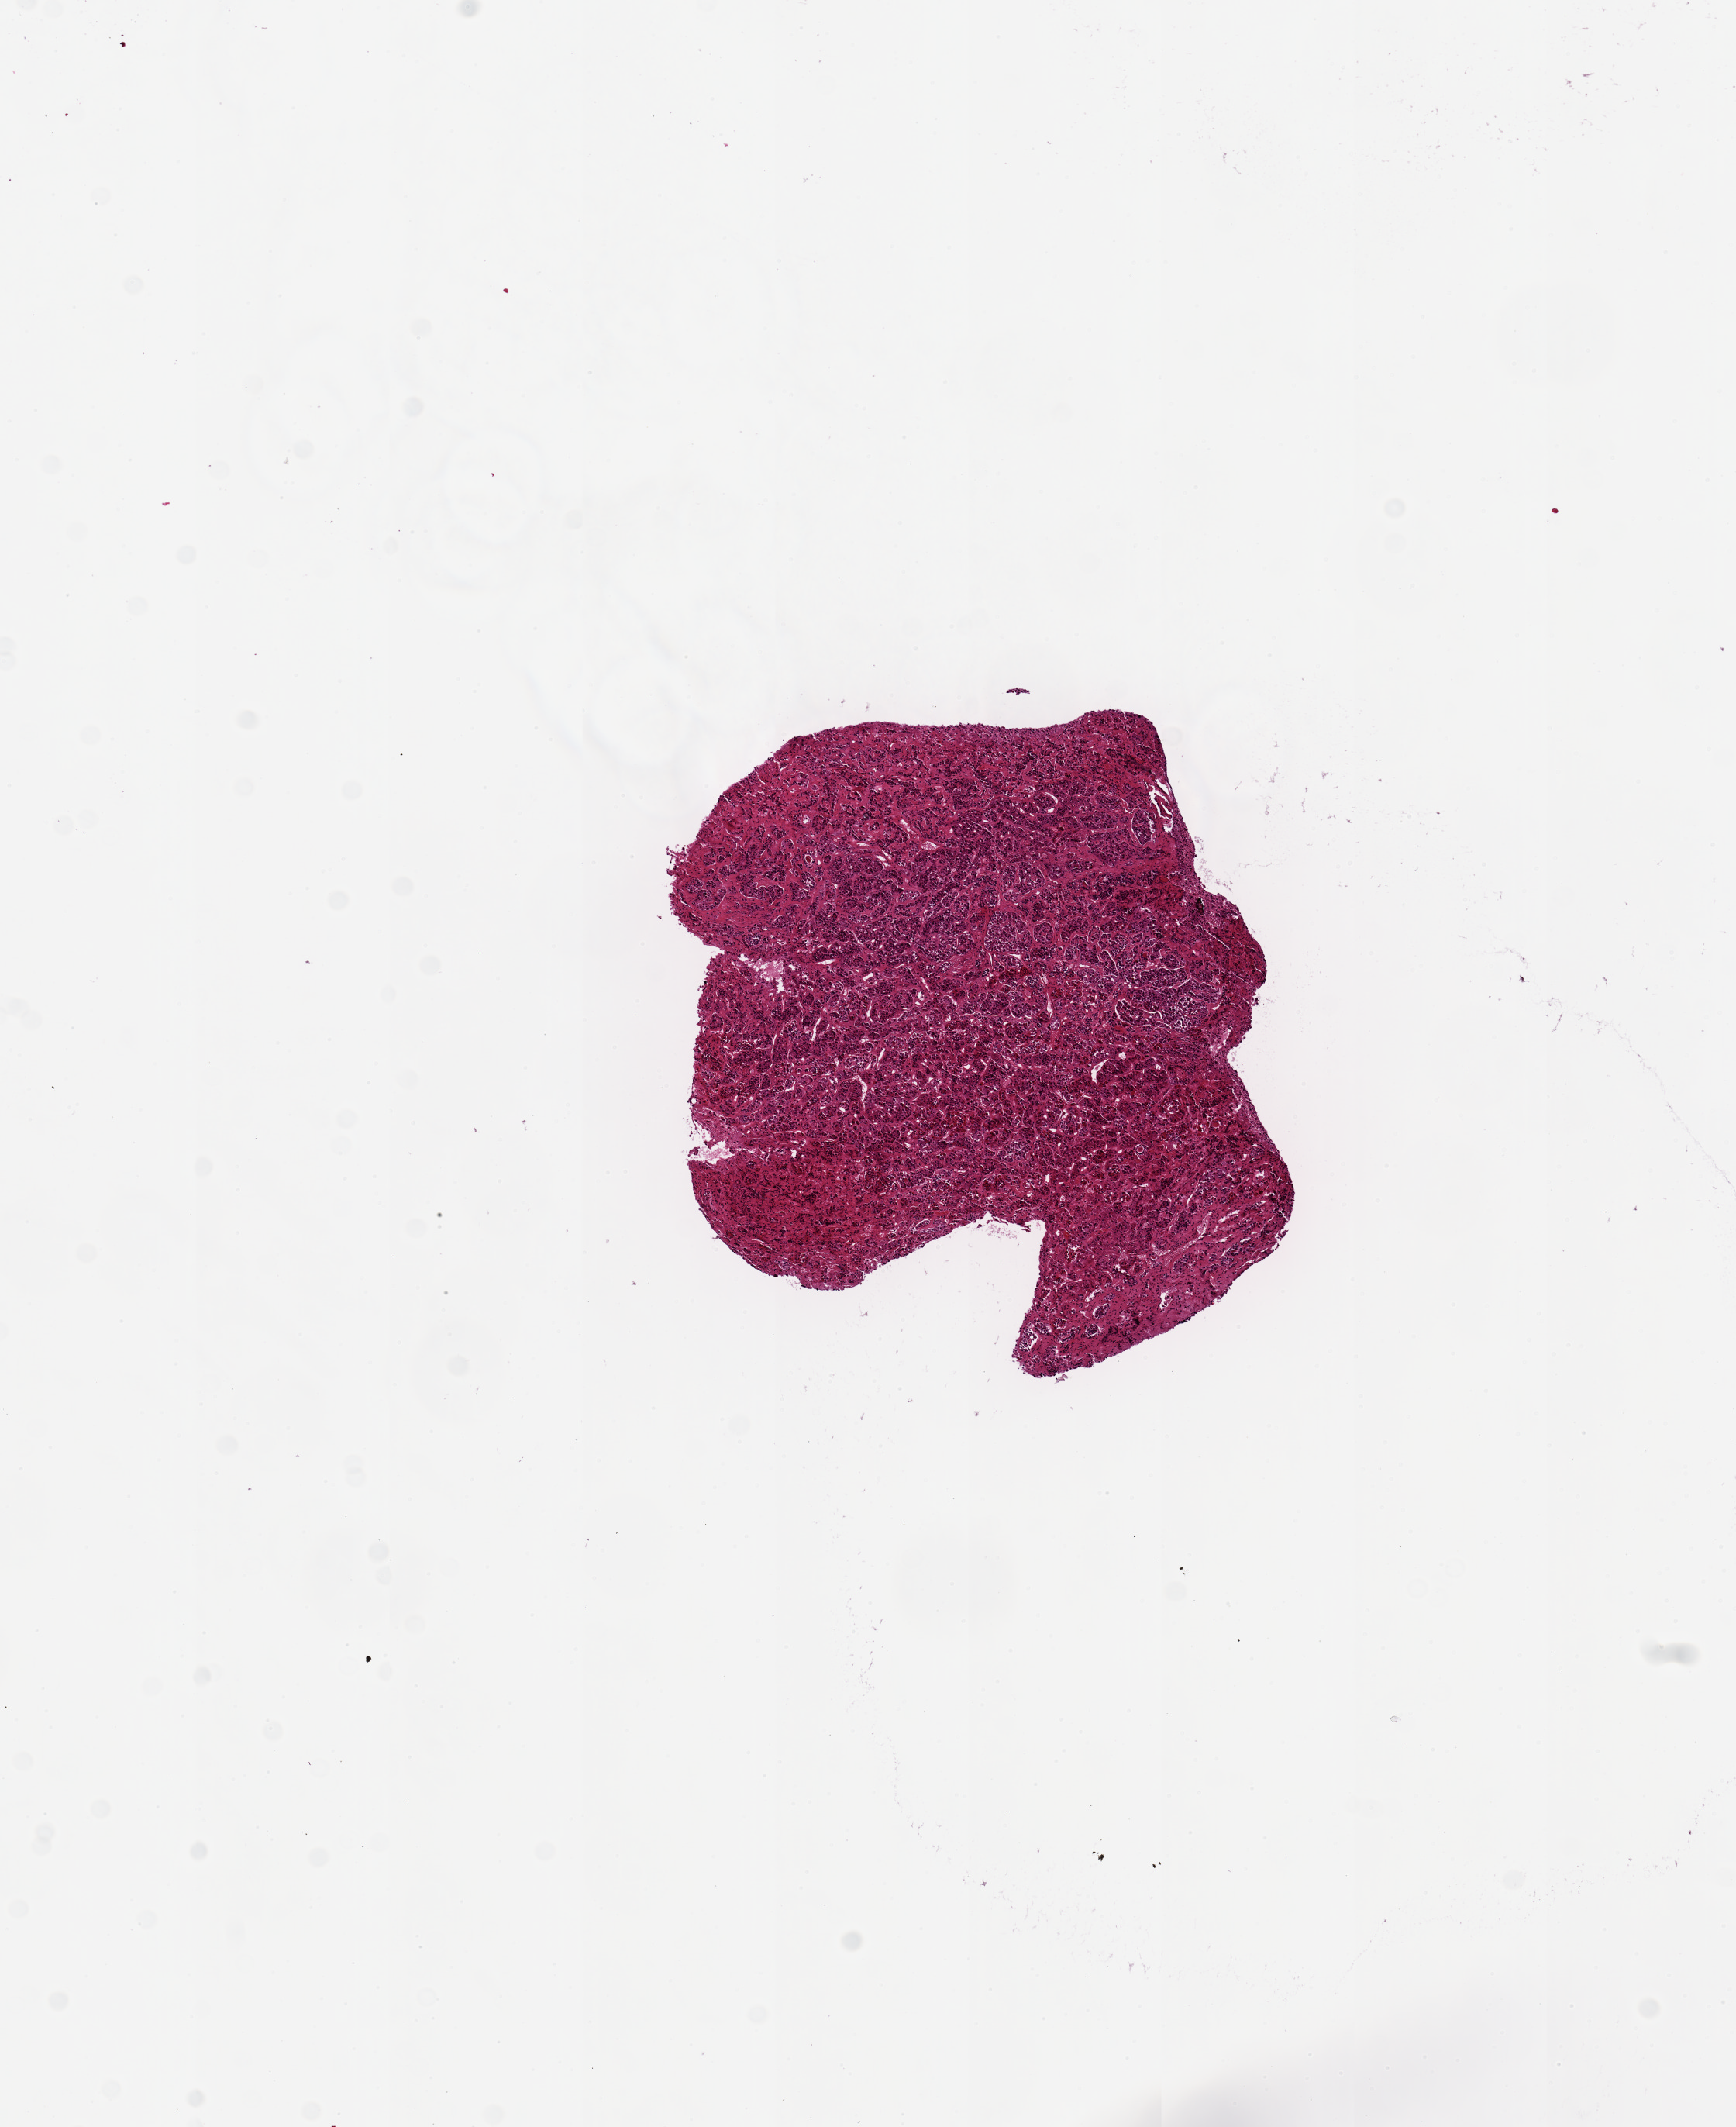
Whole-slide image, haematoxylin and eosin stain, brightfield — shown as a low-resolution overview of the whole scanned area (about 8.9 x 10.9 mm). PAXgene-fixed, paraffin-embedded tissue. Target tissue: pituitary. Tissue donor sample. Donor: male.
* pathologist's review note for this sample: 1 piece, 3x3mm; Anterior